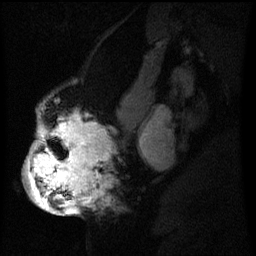
Breast MRI (dynamic contrast-enhanced), one sagittal slice; position 32 of 60 along the scan axis; dynamic contrast-enhanced series, image 2 of 3 at this slice position (ordered by acquisition); 1.5 T; TE 4.2 ms, TR 8 ms; 2.2 mm slice thickness; 256 × 256 image matrix, field of view 200 × 200 mm. Patient: female, 50 years.
Annotated regions visible in this slice (semi-automatically segmented with operator editing):
- analysis volume of interest (the breast-tissue region the enhancement analysis was run in; not a lesion): bounding box [x1, y1, x2, y2] px = [26, 112, 107, 211]
- tumour enhancement mask (voxels above the 70 % enhancement threshold inside the analysis volume of interest): [27, 118, 96, 211]